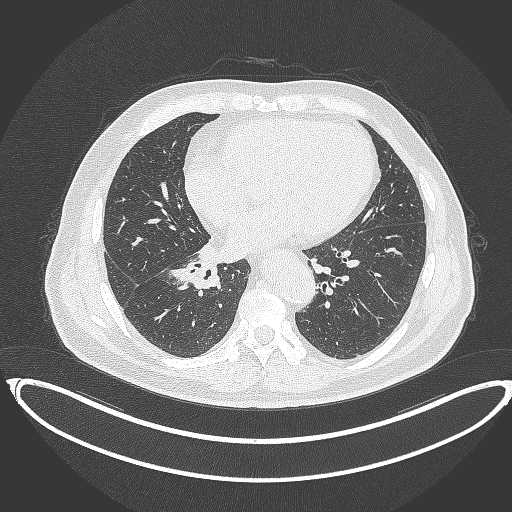
Chest CT, one axial slice; position 168 of 387 along the scan axis; 120 kVp; lung window (W 1500 / L -600 HU); 1 mm slice thickness; 512 × 512 image matrix, field of view 448 × 448 mm. Male patient, age 61 years. Case-level facts recorded for this patient, not image findings: clinical TNM (as recorded): T1b N1 M0.
Outlined on this slice (rectangle marked by the reading radiologist):
- lung tumour (recorded histology: squamous cell carcinoma): bounding box (x1, y1, x2, y2) in pixels: (171, 257, 222, 295)